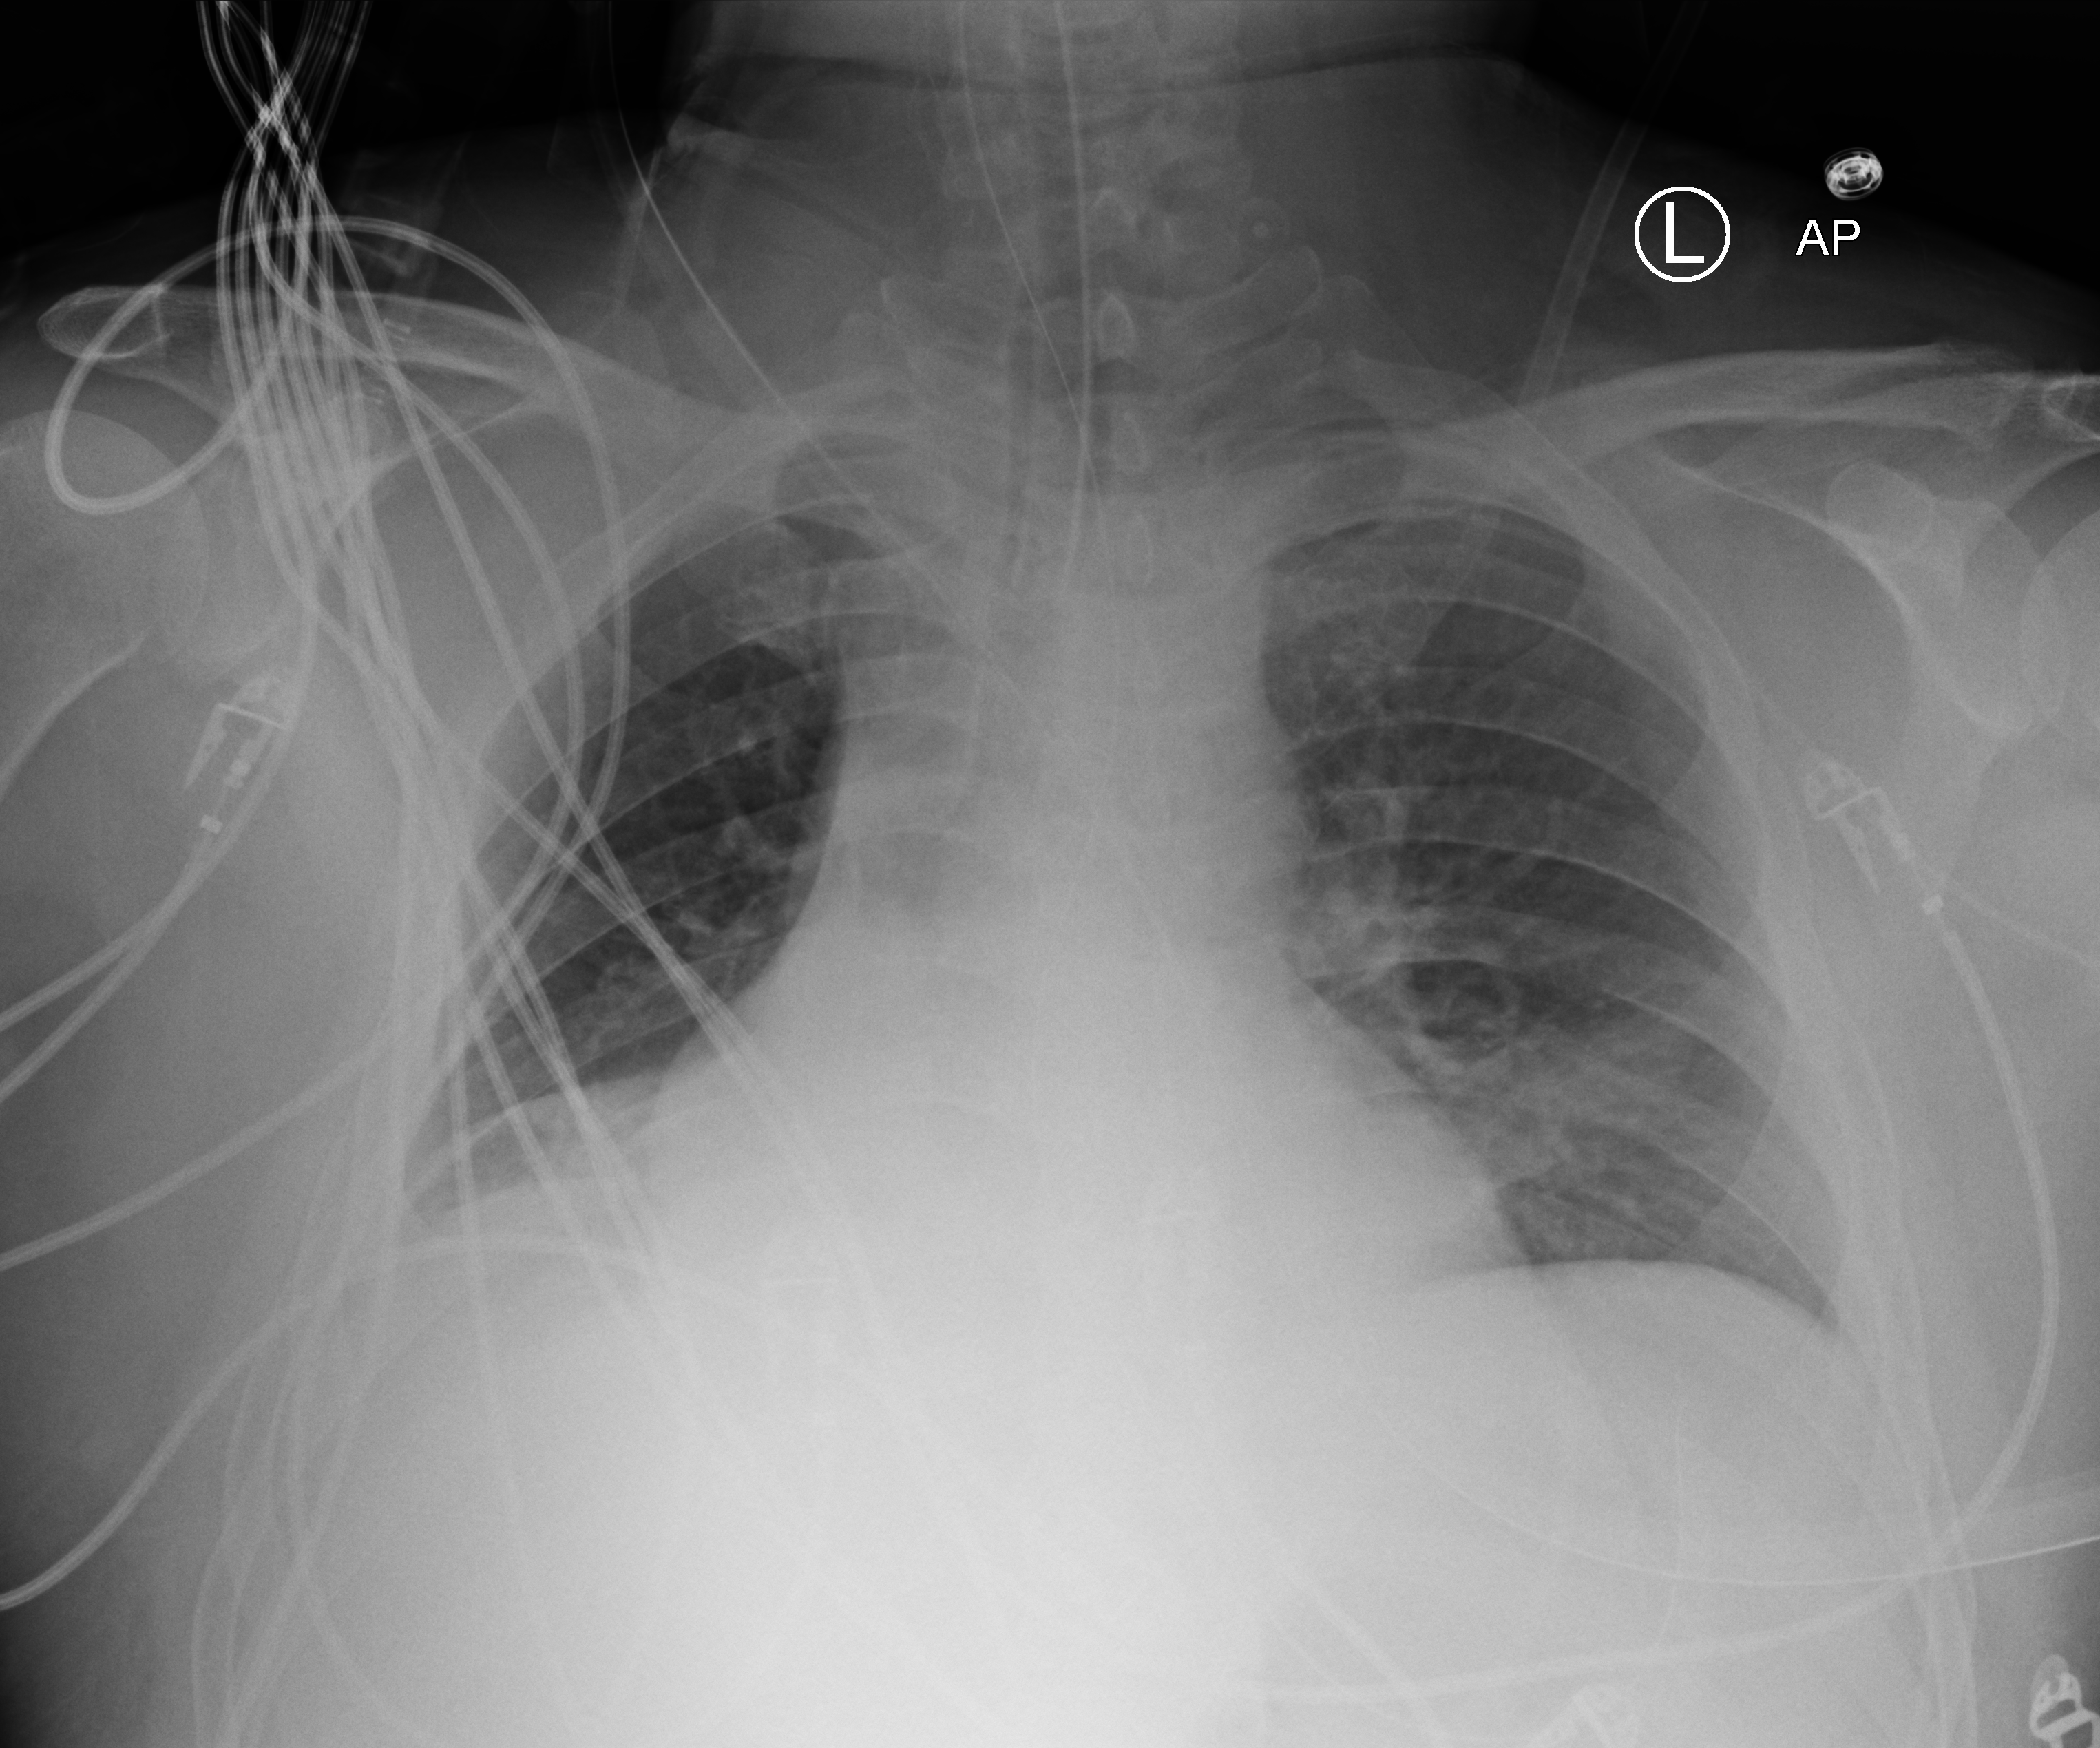
Chest X-ray (portable); anteroposterior (AP) projection. Male patient hospitalised with COVID-19, age 18–59 years.
Admission-level facts for this patient (not findings on this image; timing relative to this image not recorded): mechanically ventilated during this hospital stay: yes.